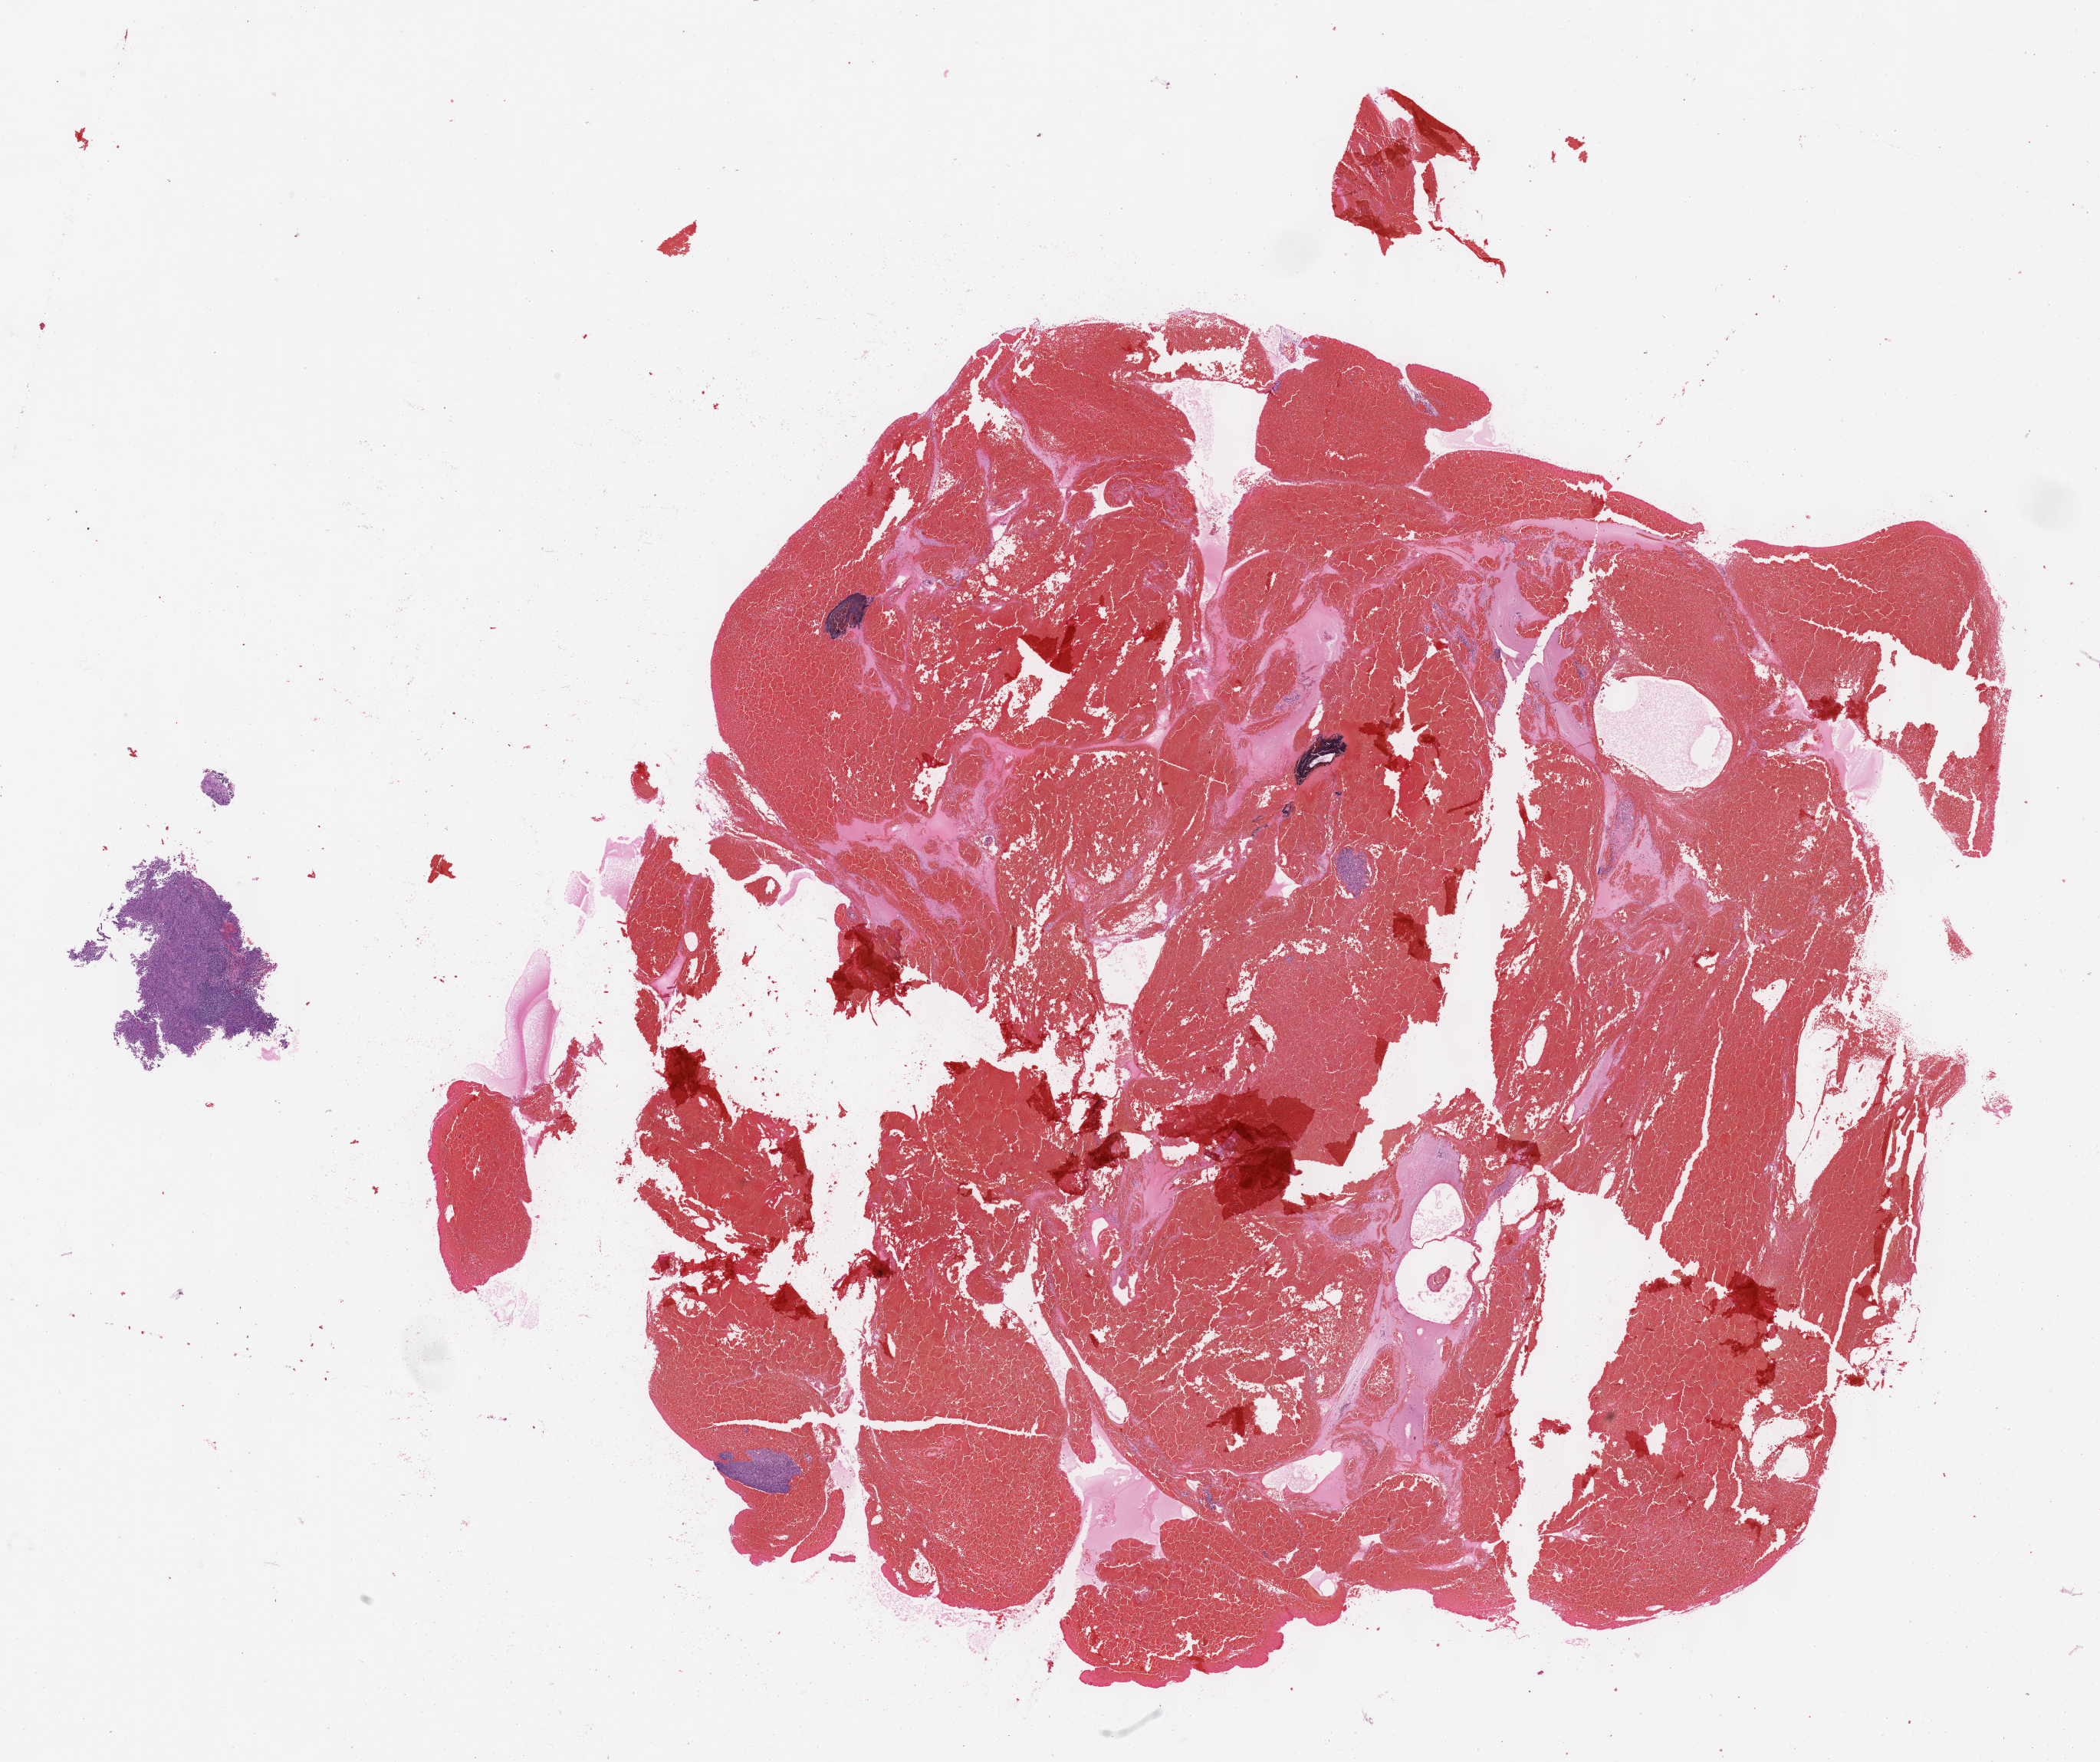
Digitized H&E tissue section (whole slide) — whole scanned area (about 22.1 x 18.6 mm) shown as a low-resolution overview. FFPE section. Sample: primary tumour, cervix. Patient: female, age at initial diagnosis 75 years. Histologic grade: G3 (poorly differentiated).
* FIGO stage: IIB
* pathologic diagnosis: Squamous cell carcinoma, NOS (cervix uteri)